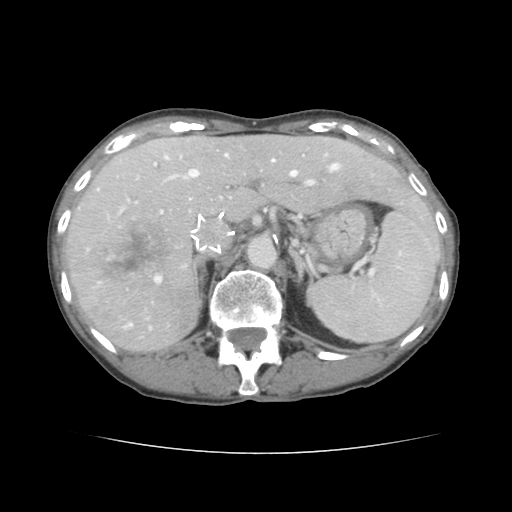
Contrast-enhanced abdominal CT, one axial slice. Position 95 of 136 along the scan axis. Intravenous contrast given. Soft-tissue window (W 400 / L 40 HU). 512 × 512 image matrix, field of view 319 × 319 mm. Female patient, age 77 years. Case-level facts recorded for this patient, not image findings: diagnosis: colorectal cancer liver metastases, imaged before liver resection; multiple liver metastases: yes; largest metastasis: 3 cm; disease in both lobes: no.
Outlined on this slice (manually delineated by an expert):
- hepatic veins: bounding box <124,154,338,329> (left, top, right, bottom; pixels)
- liver: <67,136,434,352>
- planned liver remnant (the part of the liver to remain after resection): <154,136,434,234>
- portal vein (with intrahepatic branches): <98,163,317,282>
- liver metastasis: <95,219,175,284>